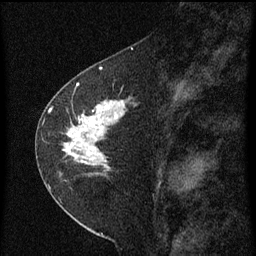
Breast MRI (dynamic contrast-enhanced), one sagittal slice. Position 31 of 60 along the scan axis. Dynamic contrast-enhanced series, image 2 of 3 at this slice position (ordered by acquisition). 1.5 T. TE 4.2 ms, TR 8 ms. 2 mm slice thickness. 256 × 256 image matrix. Female patient, age 47 years.
Structures marked on this image (semi-automatically segmented with operator editing):
- analysis volume of interest (the breast-tissue region the enhancement analysis was run in; not a lesion): bounding box (x1, y1, x2, y2) in pixels: (44, 84, 141, 199)
- tumour enhancement mask (voxels above the 70 % enhancement threshold inside the analysis volume of interest): (64, 84, 125, 161)